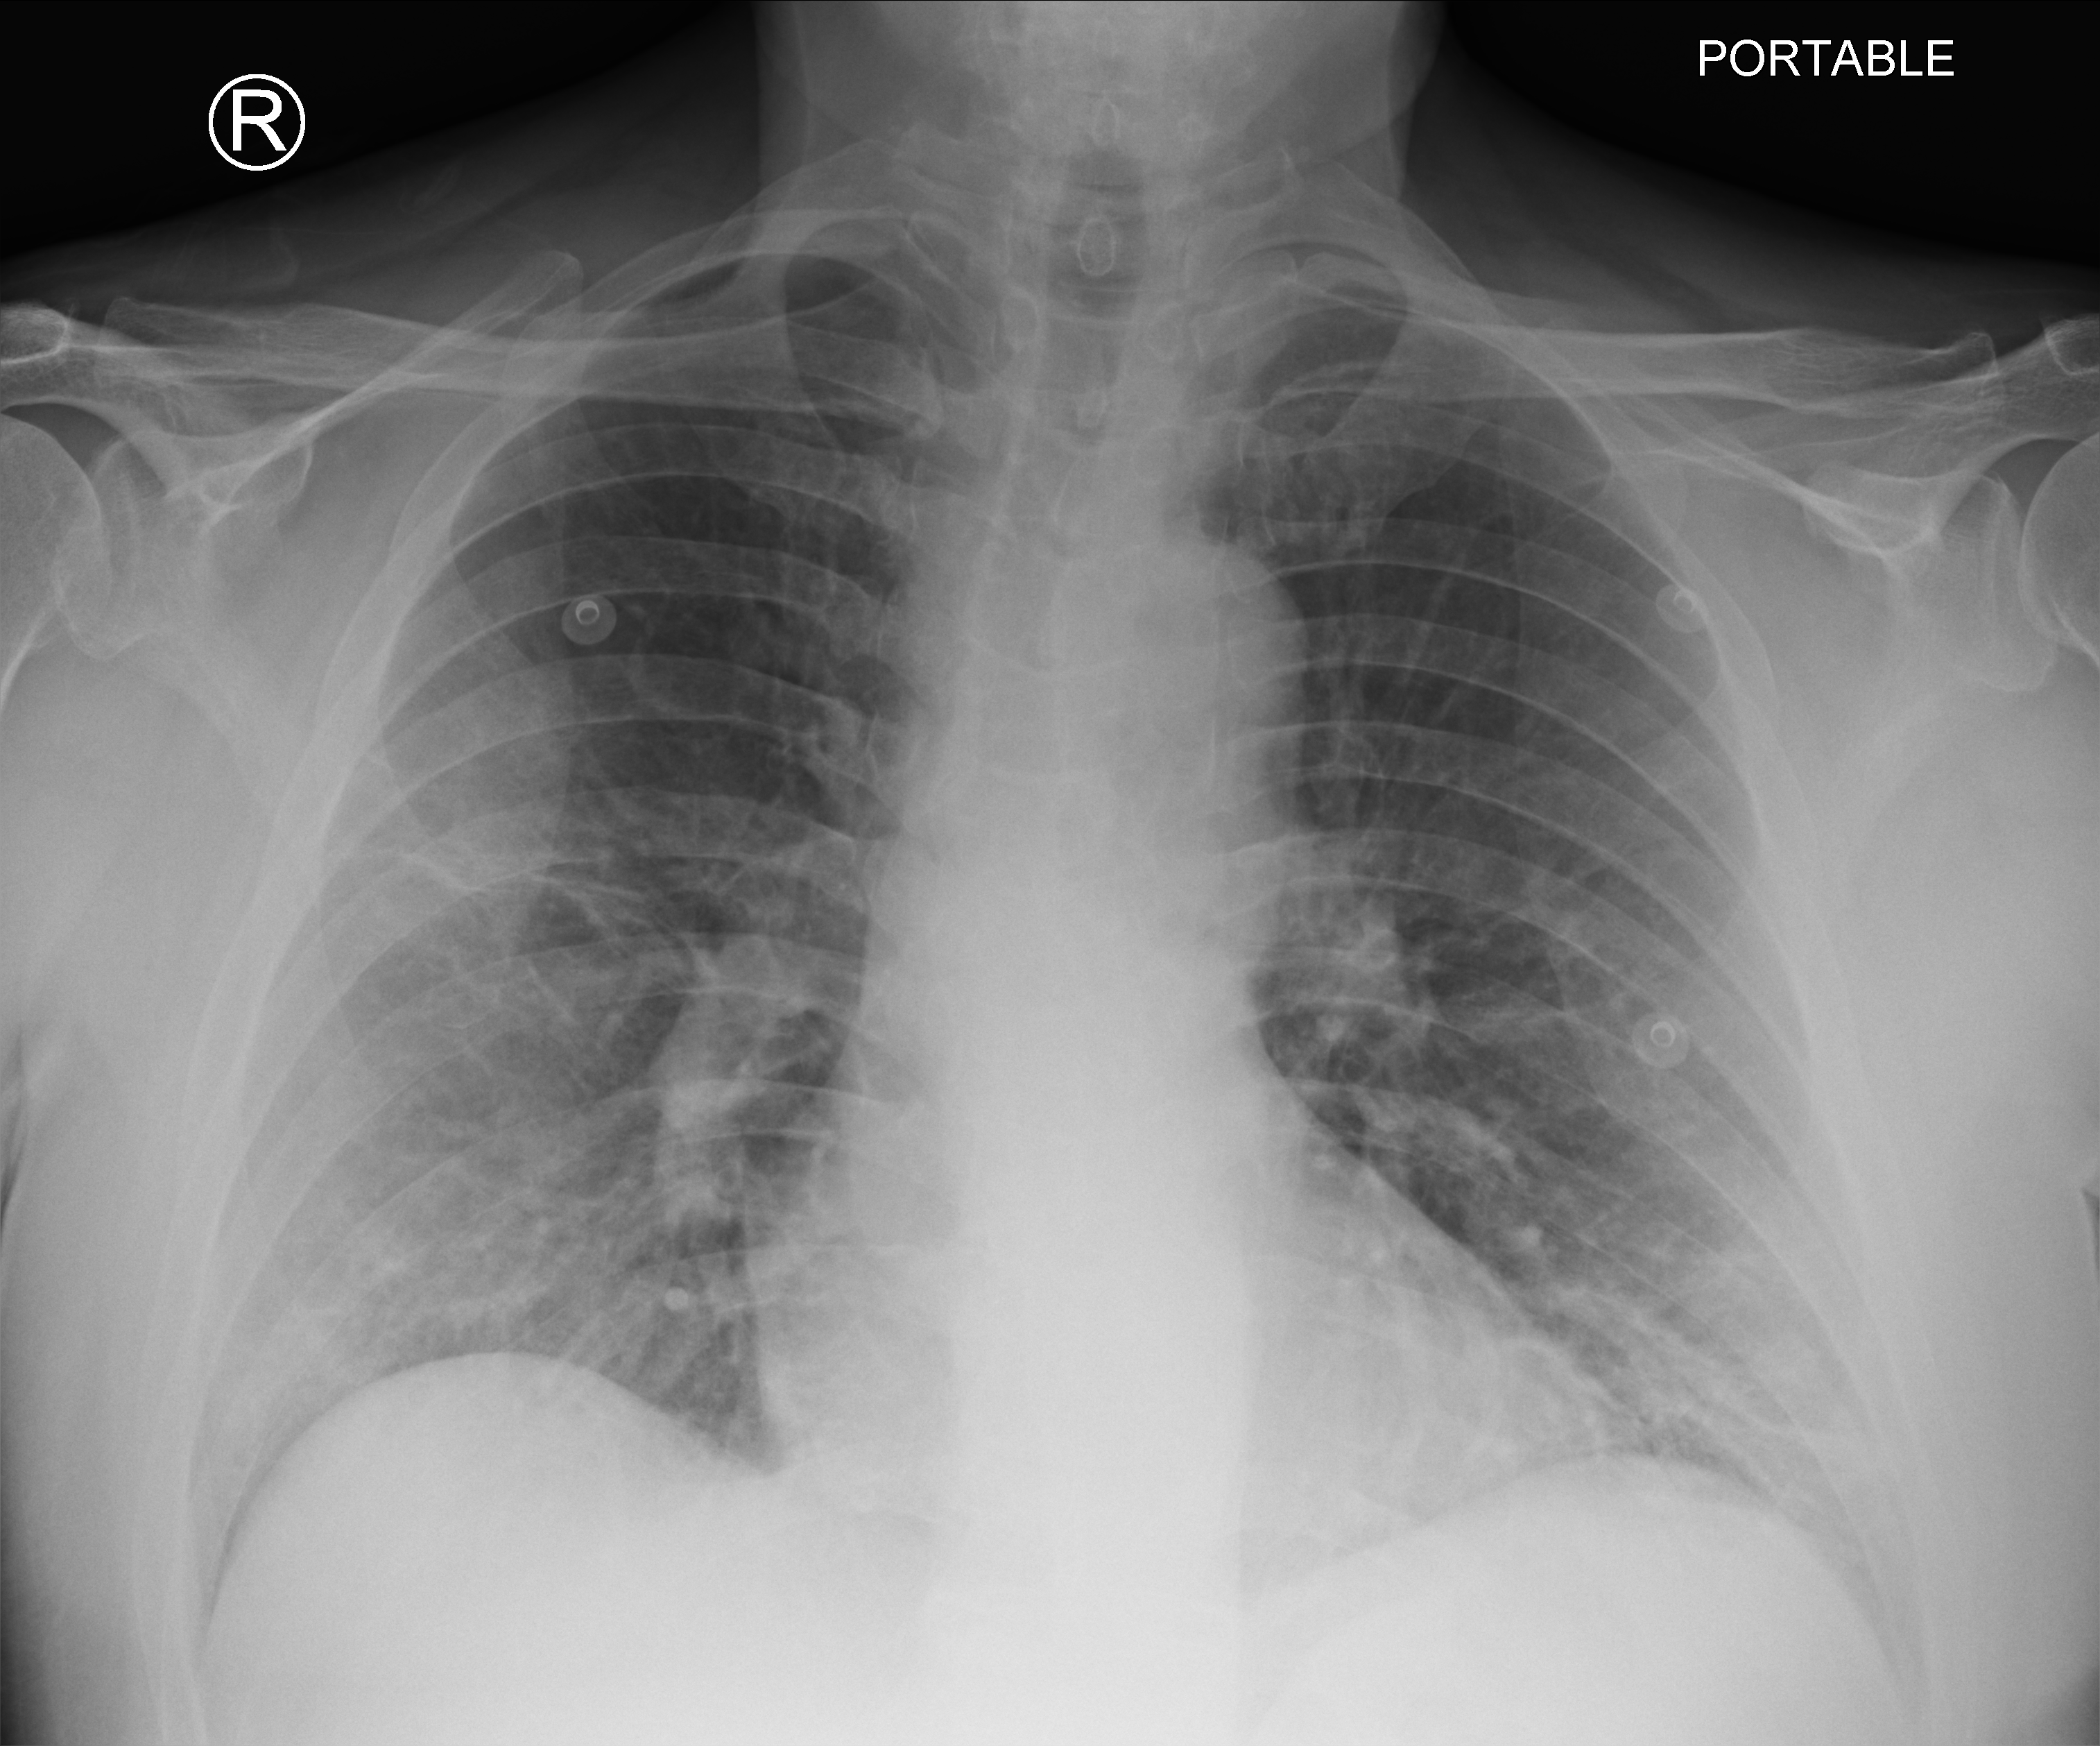
Bedside chest radiograph (computed radiography). Patient hospitalised with COVID-19; male, aged 18–59 years.
Admission-level facts for this patient (not findings on this image; timing relative to this image not recorded):
- admitted to intensive care during this hospital stay: no
- mechanically ventilated during this hospital stay: no